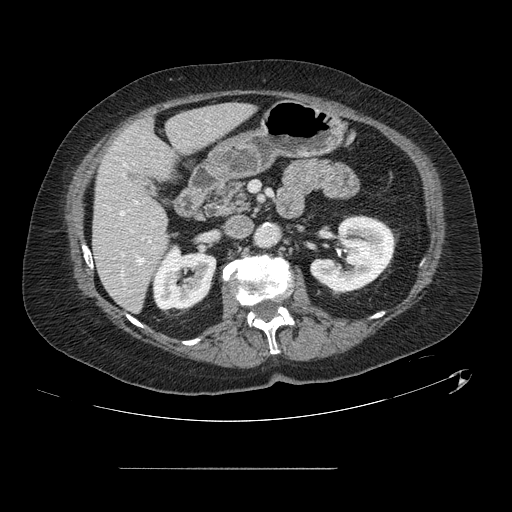
Contrast-enhanced abdominal CT, one axial slice. Slice 52 of 148 in the series (ordered by position). 120 kVp. Intravenous contrast given. Soft-tissue window (W 400 / L 40 HU). 2.5 mm slice thickness. 512 × 512 image matrix, field of view 439 × 439 mm. Female patient, age 75 years. Case-level facts recorded for this patient, not image findings: diagnosis: colorectal cancer liver metastases, imaged before liver resection; multiple liver metastases: no; largest metastasis: 2.4 cm; disease in both lobes: no.
Structures marked on this image (outlined manually by an expert reader):
- hepatic veins: box from (x=120, y=211) to (x=143, y=264) px
- liver: (x=94, y=103)–(x=254, y=311)
- planned liver remnant (the part of the liver to remain after resection): (x=94, y=103)–(x=253, y=311)